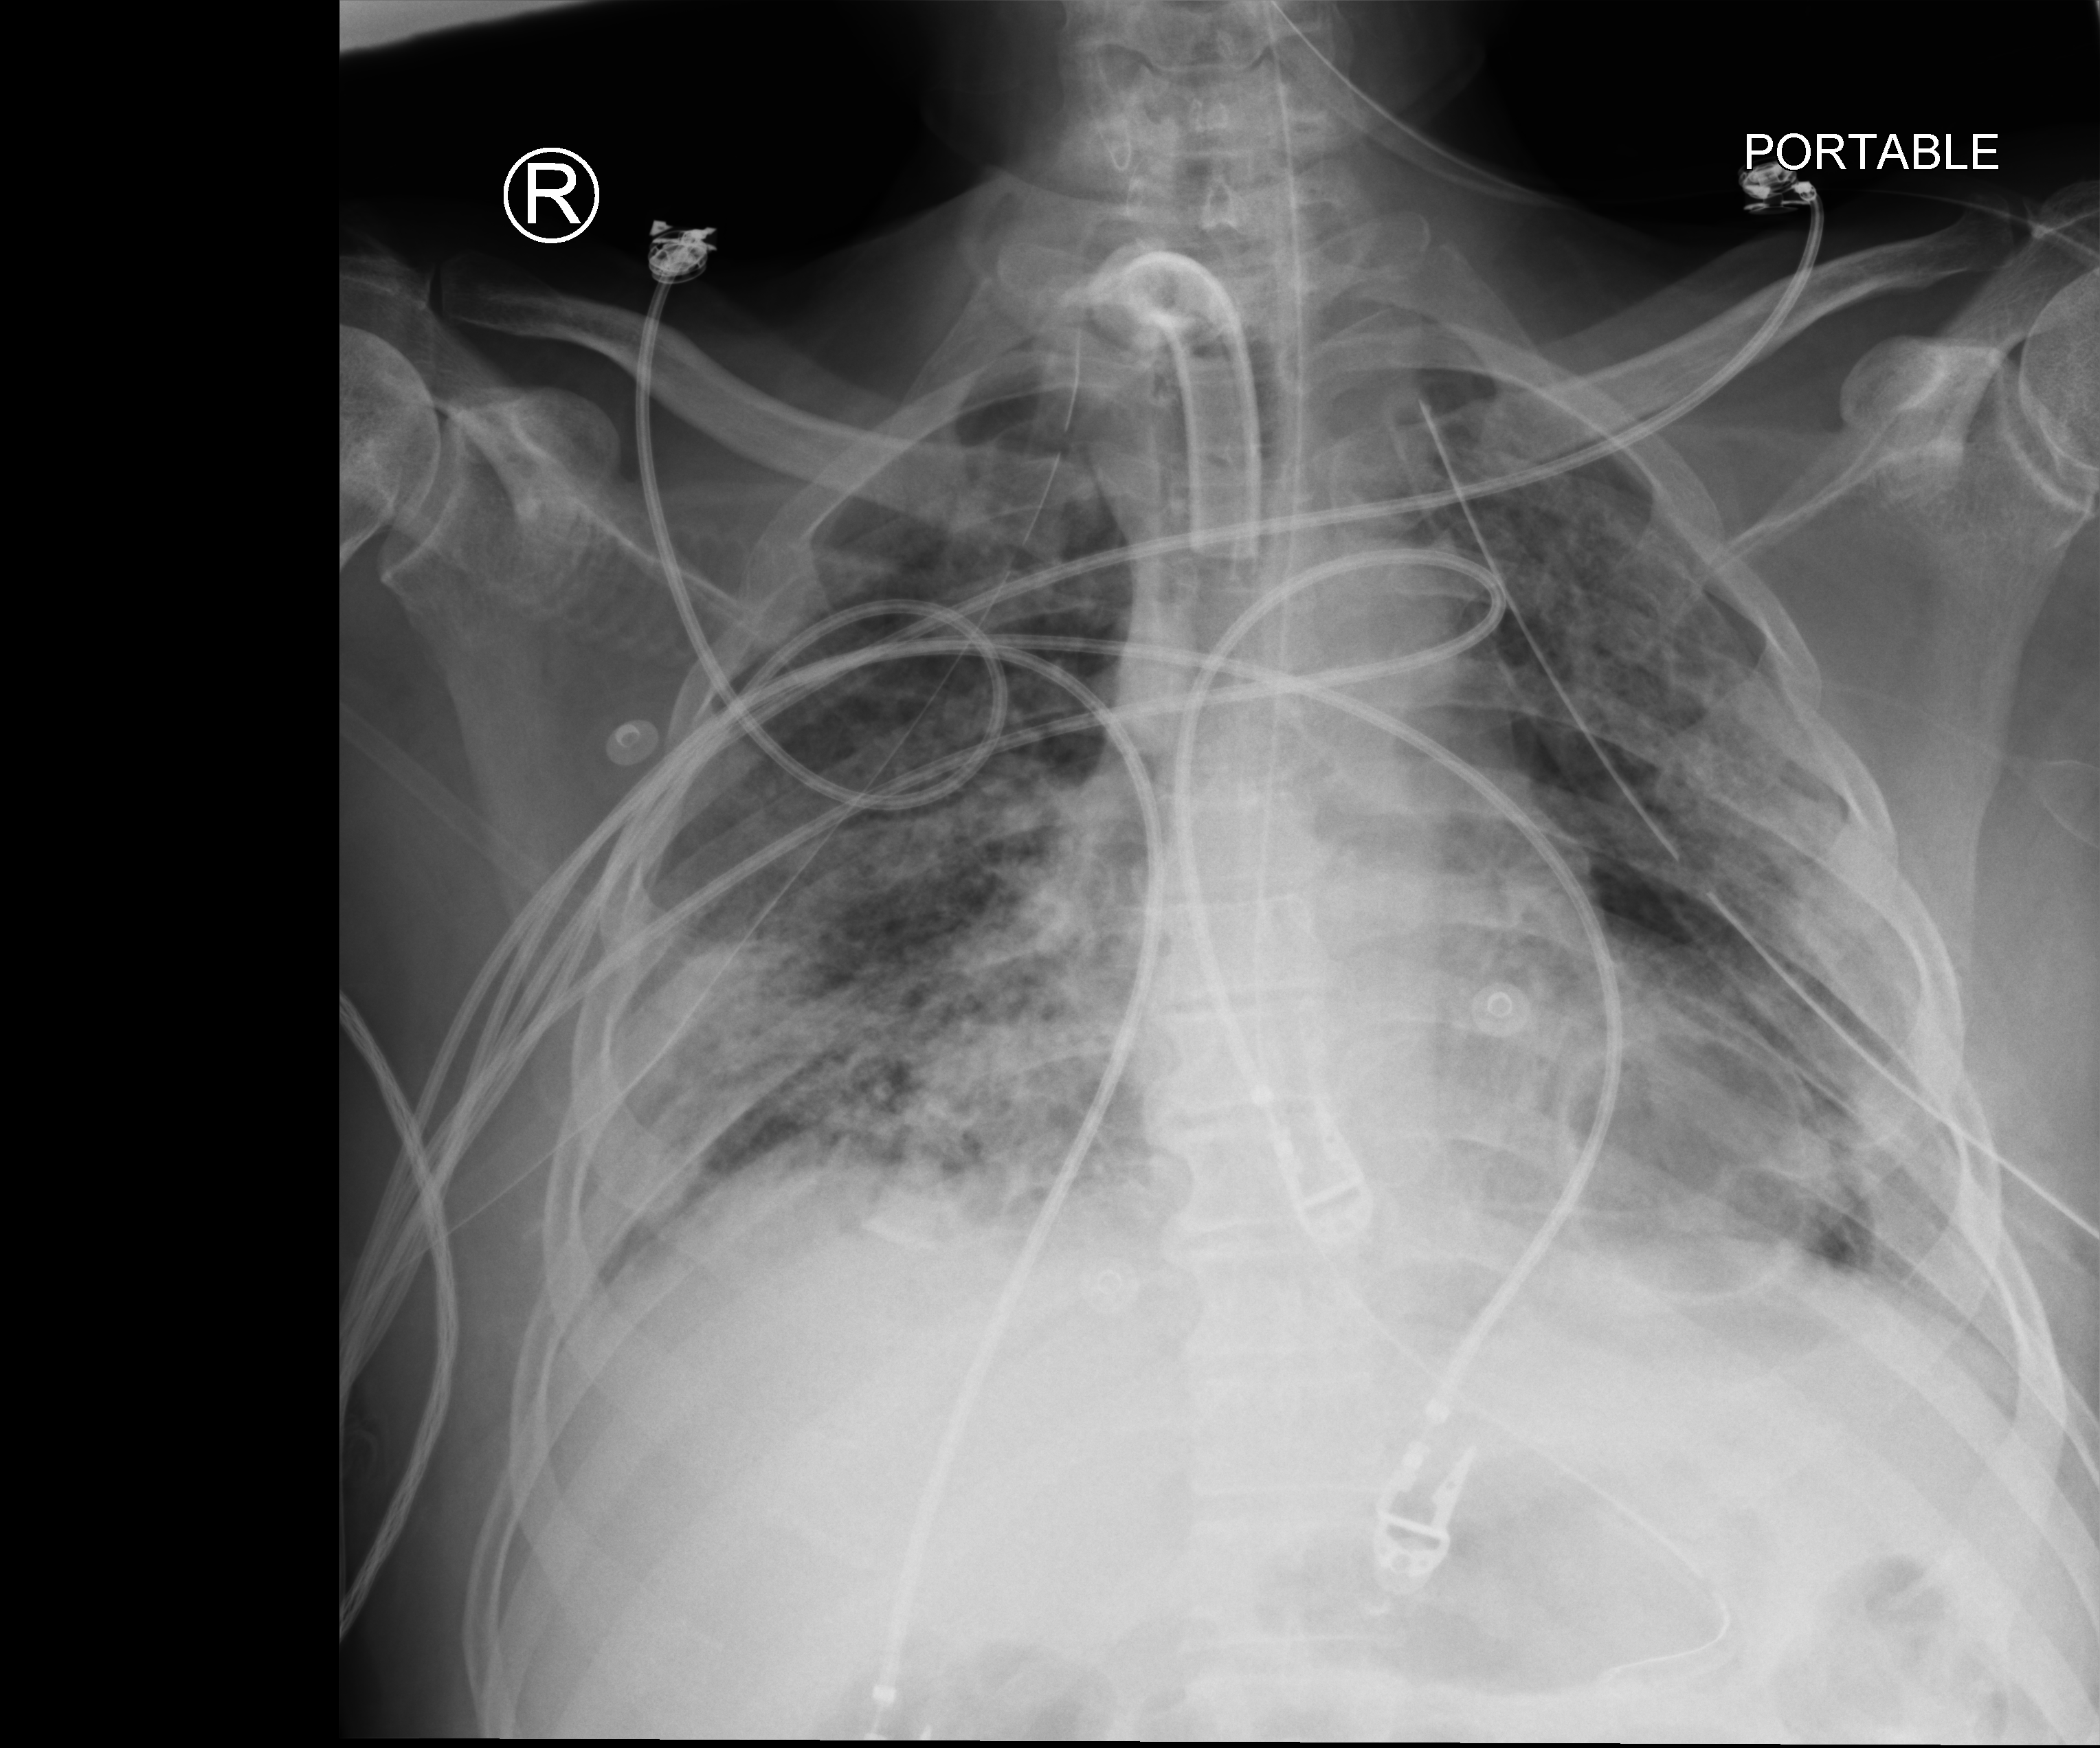
Portable chest radiograph, anteroposterior (AP) projection. Patient hospitalised with COVID-19; male, aged 18–59 years.
From the hospital-stay record, not from the radiograph (when in the stay this image was taken is not recorded):
- diabetes (admission record): no
- mechanically ventilated during this hospital stay: yes